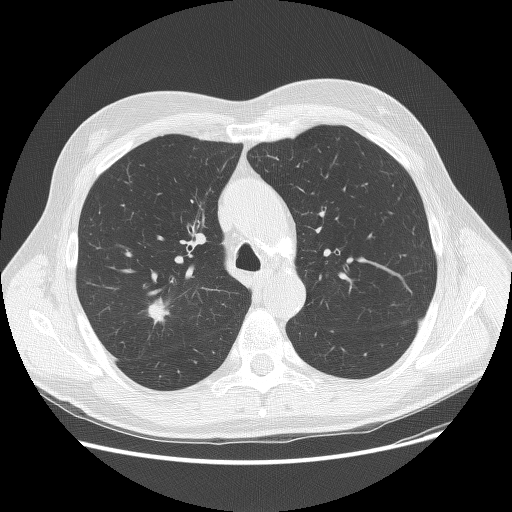
Chest CT (low-dose screening protocol), one axial image. First (baseline) screen. Lung window (W 1500 / L -600 HU). 2.5 mm slice thickness. 120 kVp. Slice 49 of 156 in the series. Male, age 70 years at enrolment. Current smoker at enrolment.
Expert-annotated lung lesion, bounding box <130,283,192,339> (left, top, right, bottom; pixels). The screening reader recorded 2 non-calcified nodules or masses ≥4 mm on this exam (right upper lobe, left lower lobe); which of them this box marks is not recorded. Official screen result: positive, change unspecified: nodule(s) >= 4 mm or enlarging nodule(s), mass(es), or other non-specific abnormalities suspicious for lung cancer. Lung cancer was diagnosed 15 days after this screen: adenocarcinoma, NOS, right upper lobe, poorly differentiated (G3), stage IIA (AJCC 6th edition), 23 mm at pathology.